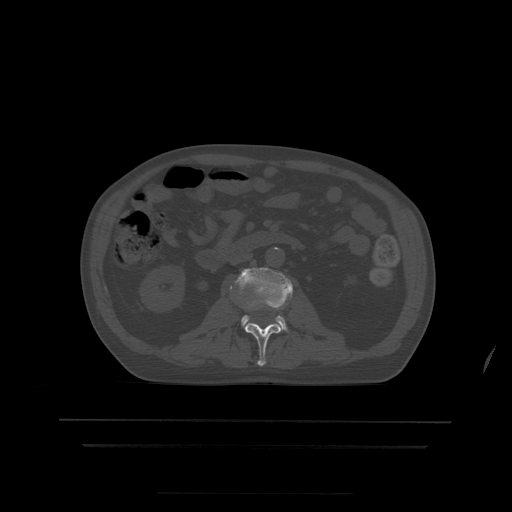
CT including the spine, one axial slice; slice 135 of 522 in the series (ordered by position); bone window (W 1800 / L 400 HU); 512 × 512 image matrix. Patient age 68 years. Case-level facts recorded for this patient, not image findings: primary cancer: urothelial.
Annotated regions visible in this slice (semi-automatic segmentation, software-assisted and operator-edited):
- L2 vertebra: bounding box (x1, y1, x2, y2) in pixels: (245, 308, 281, 367)
- L3 vertebra: (231, 268, 294, 332)